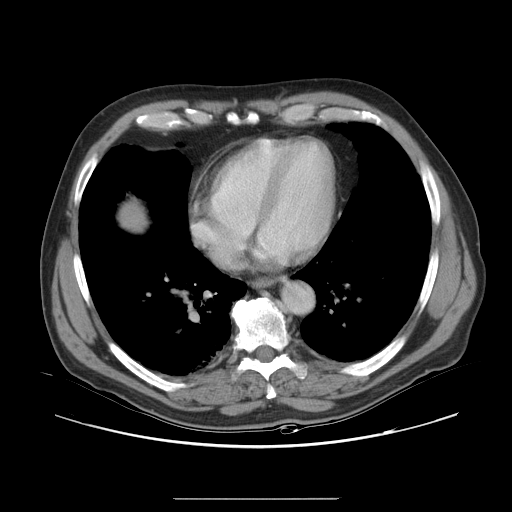
Contrast-enhanced abdominal CT, one axial slice; slice 34 of 40 in the series (ordered by position); 120 kVp; intravenous contrast given; soft-tissue window (W 400 / L 40 HU); 5 mm slice thickness; 512 × 512 image matrix. Male patient, age 64 years. From the clinical record (not read from this slice): diagnosis: colorectal cancer liver metastases, imaged before liver resection; multiple liver metastases: yes; largest metastasis: 3.2 cm; chemotherapy before resection: yes.
Outlined on this slice (manually delineated by an expert):
- liver: box from (x=124, y=208) to (x=143, y=227) px
- planned liver remnant (the part of the liver to remain after resection): (x=124, y=209)–(x=143, y=227)